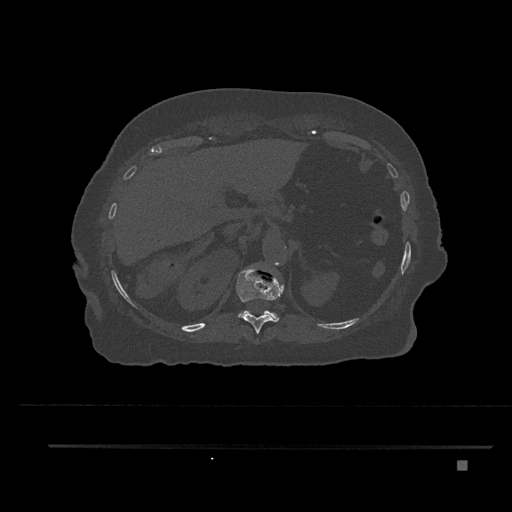
CT including the spine, one axial slice; slice 301 of 797 in the series (ordered by position); 120 kVp; bone window (W 1800 / L 400 HU); 512 × 512 image matrix. Patient: female, 76 years. From the clinical record (not read from this slice): primary cancer: lung; vertebrae with lytic lesions (as recorded): T11, L3.
Outlined on this slice (semi-automatic segmentation, software-assisted and operator-edited):
- T11 vertebra: box from (x=236, y=266) to (x=284, y=333) px
- T12 vertebra: (x=238, y=311)–(x=279, y=321)